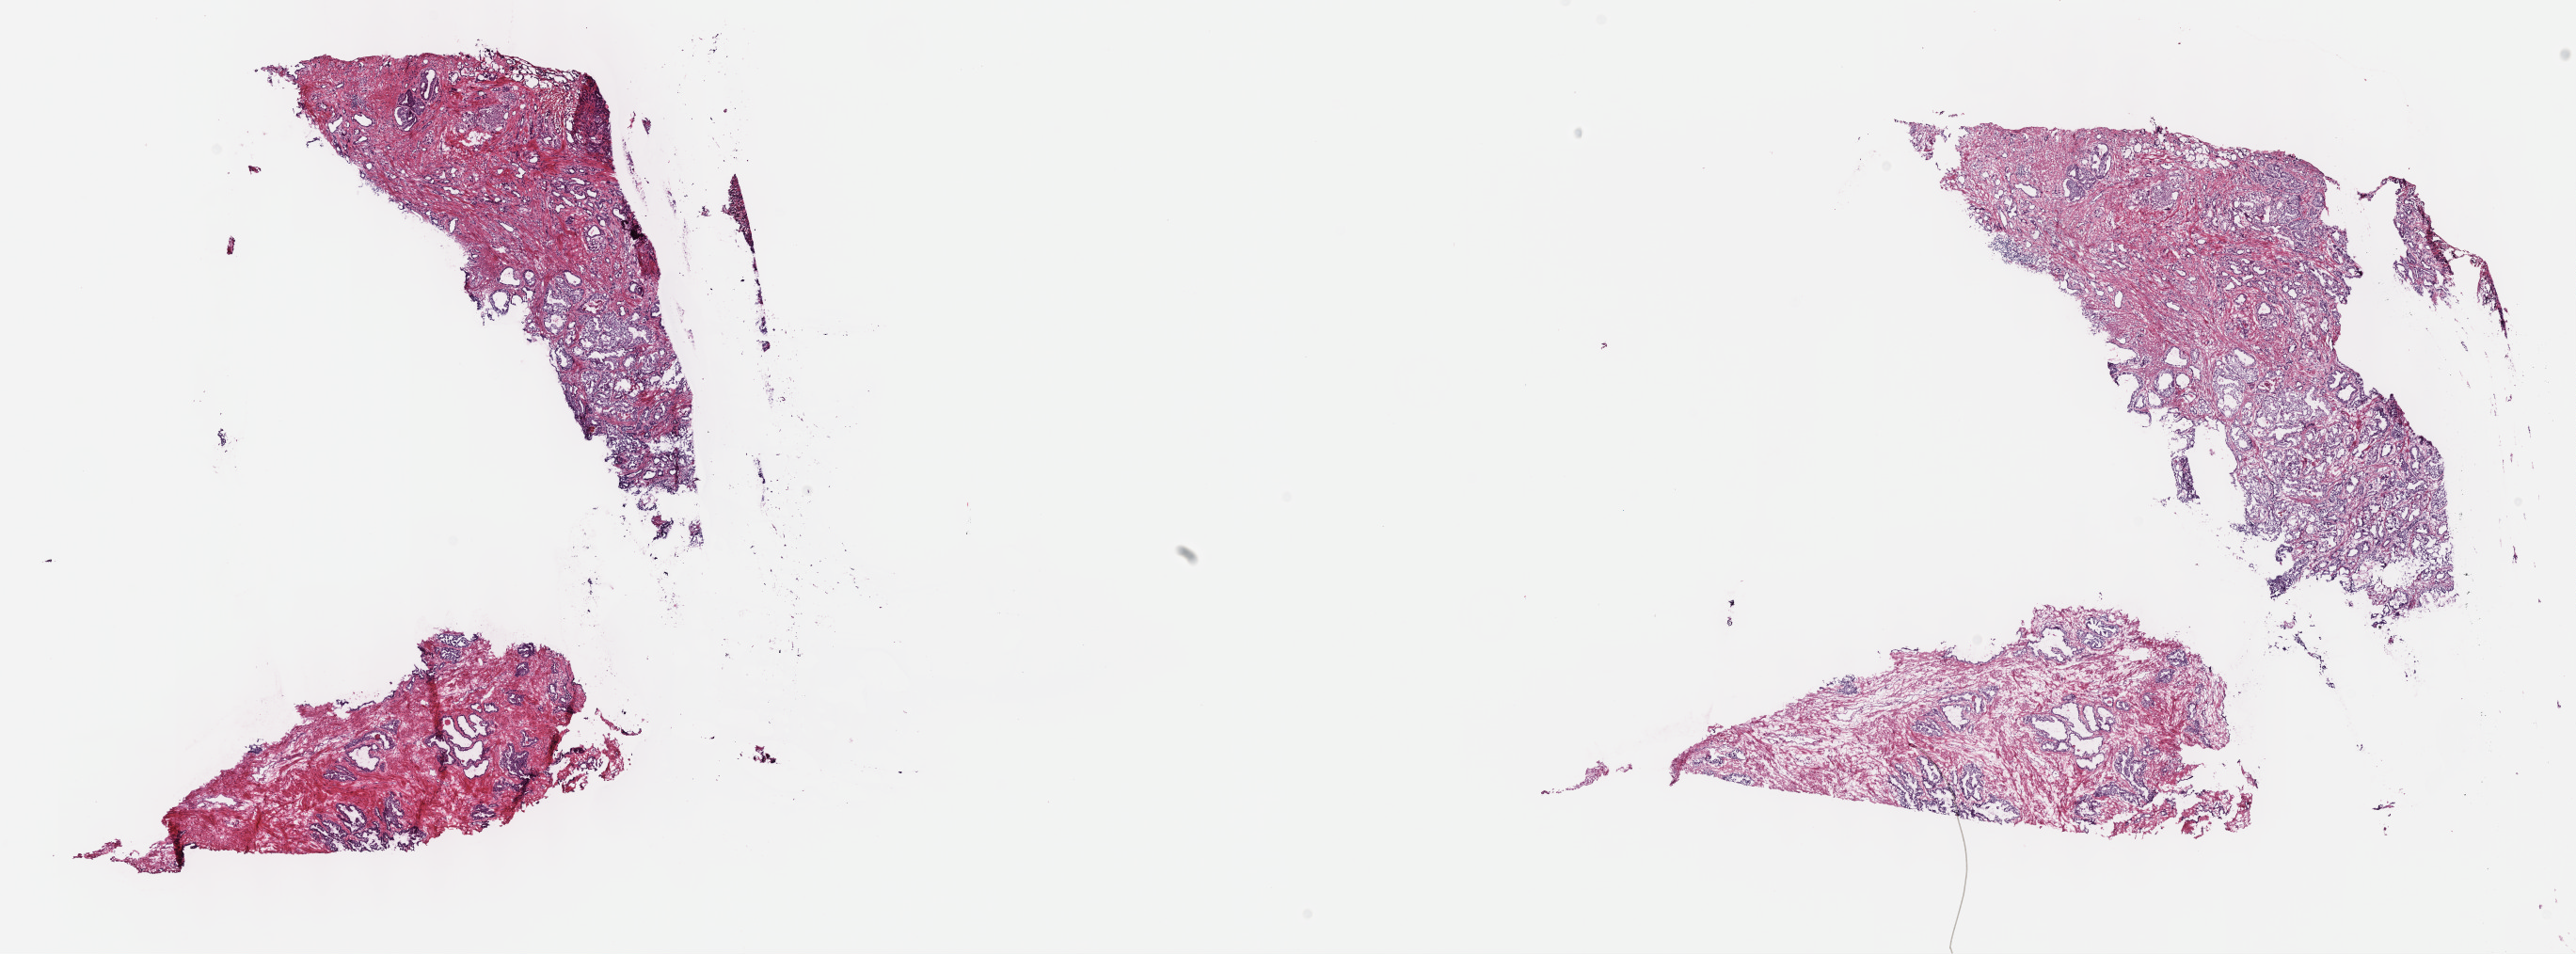
Whole-slide histology image, Hematoxylin and eosin (H&E) stained, a low-resolution overview of the entire scanned area, about 22.1 x 8.2 mm; frozen section; prostate, primary tumour sample. Male, age 58 years at initial diagnosis. Gleason score: 7 (3+4). Composition of this section per pathologist review: tumour cells 70%, tumour nuclei 70%, normal cells 0%, stromal cells 30%, necrosis 0%. Inflammatory infiltration, as recorded: lymphocyte infiltration 40%, monocyte infiltration 20%, neutrophil infiltration 20%.
Histologic diagnosis: Adenocarcinoma, NOS. Laterality: bilateral. Lymph nodes positive (case pathology): 0 of 48 examined.